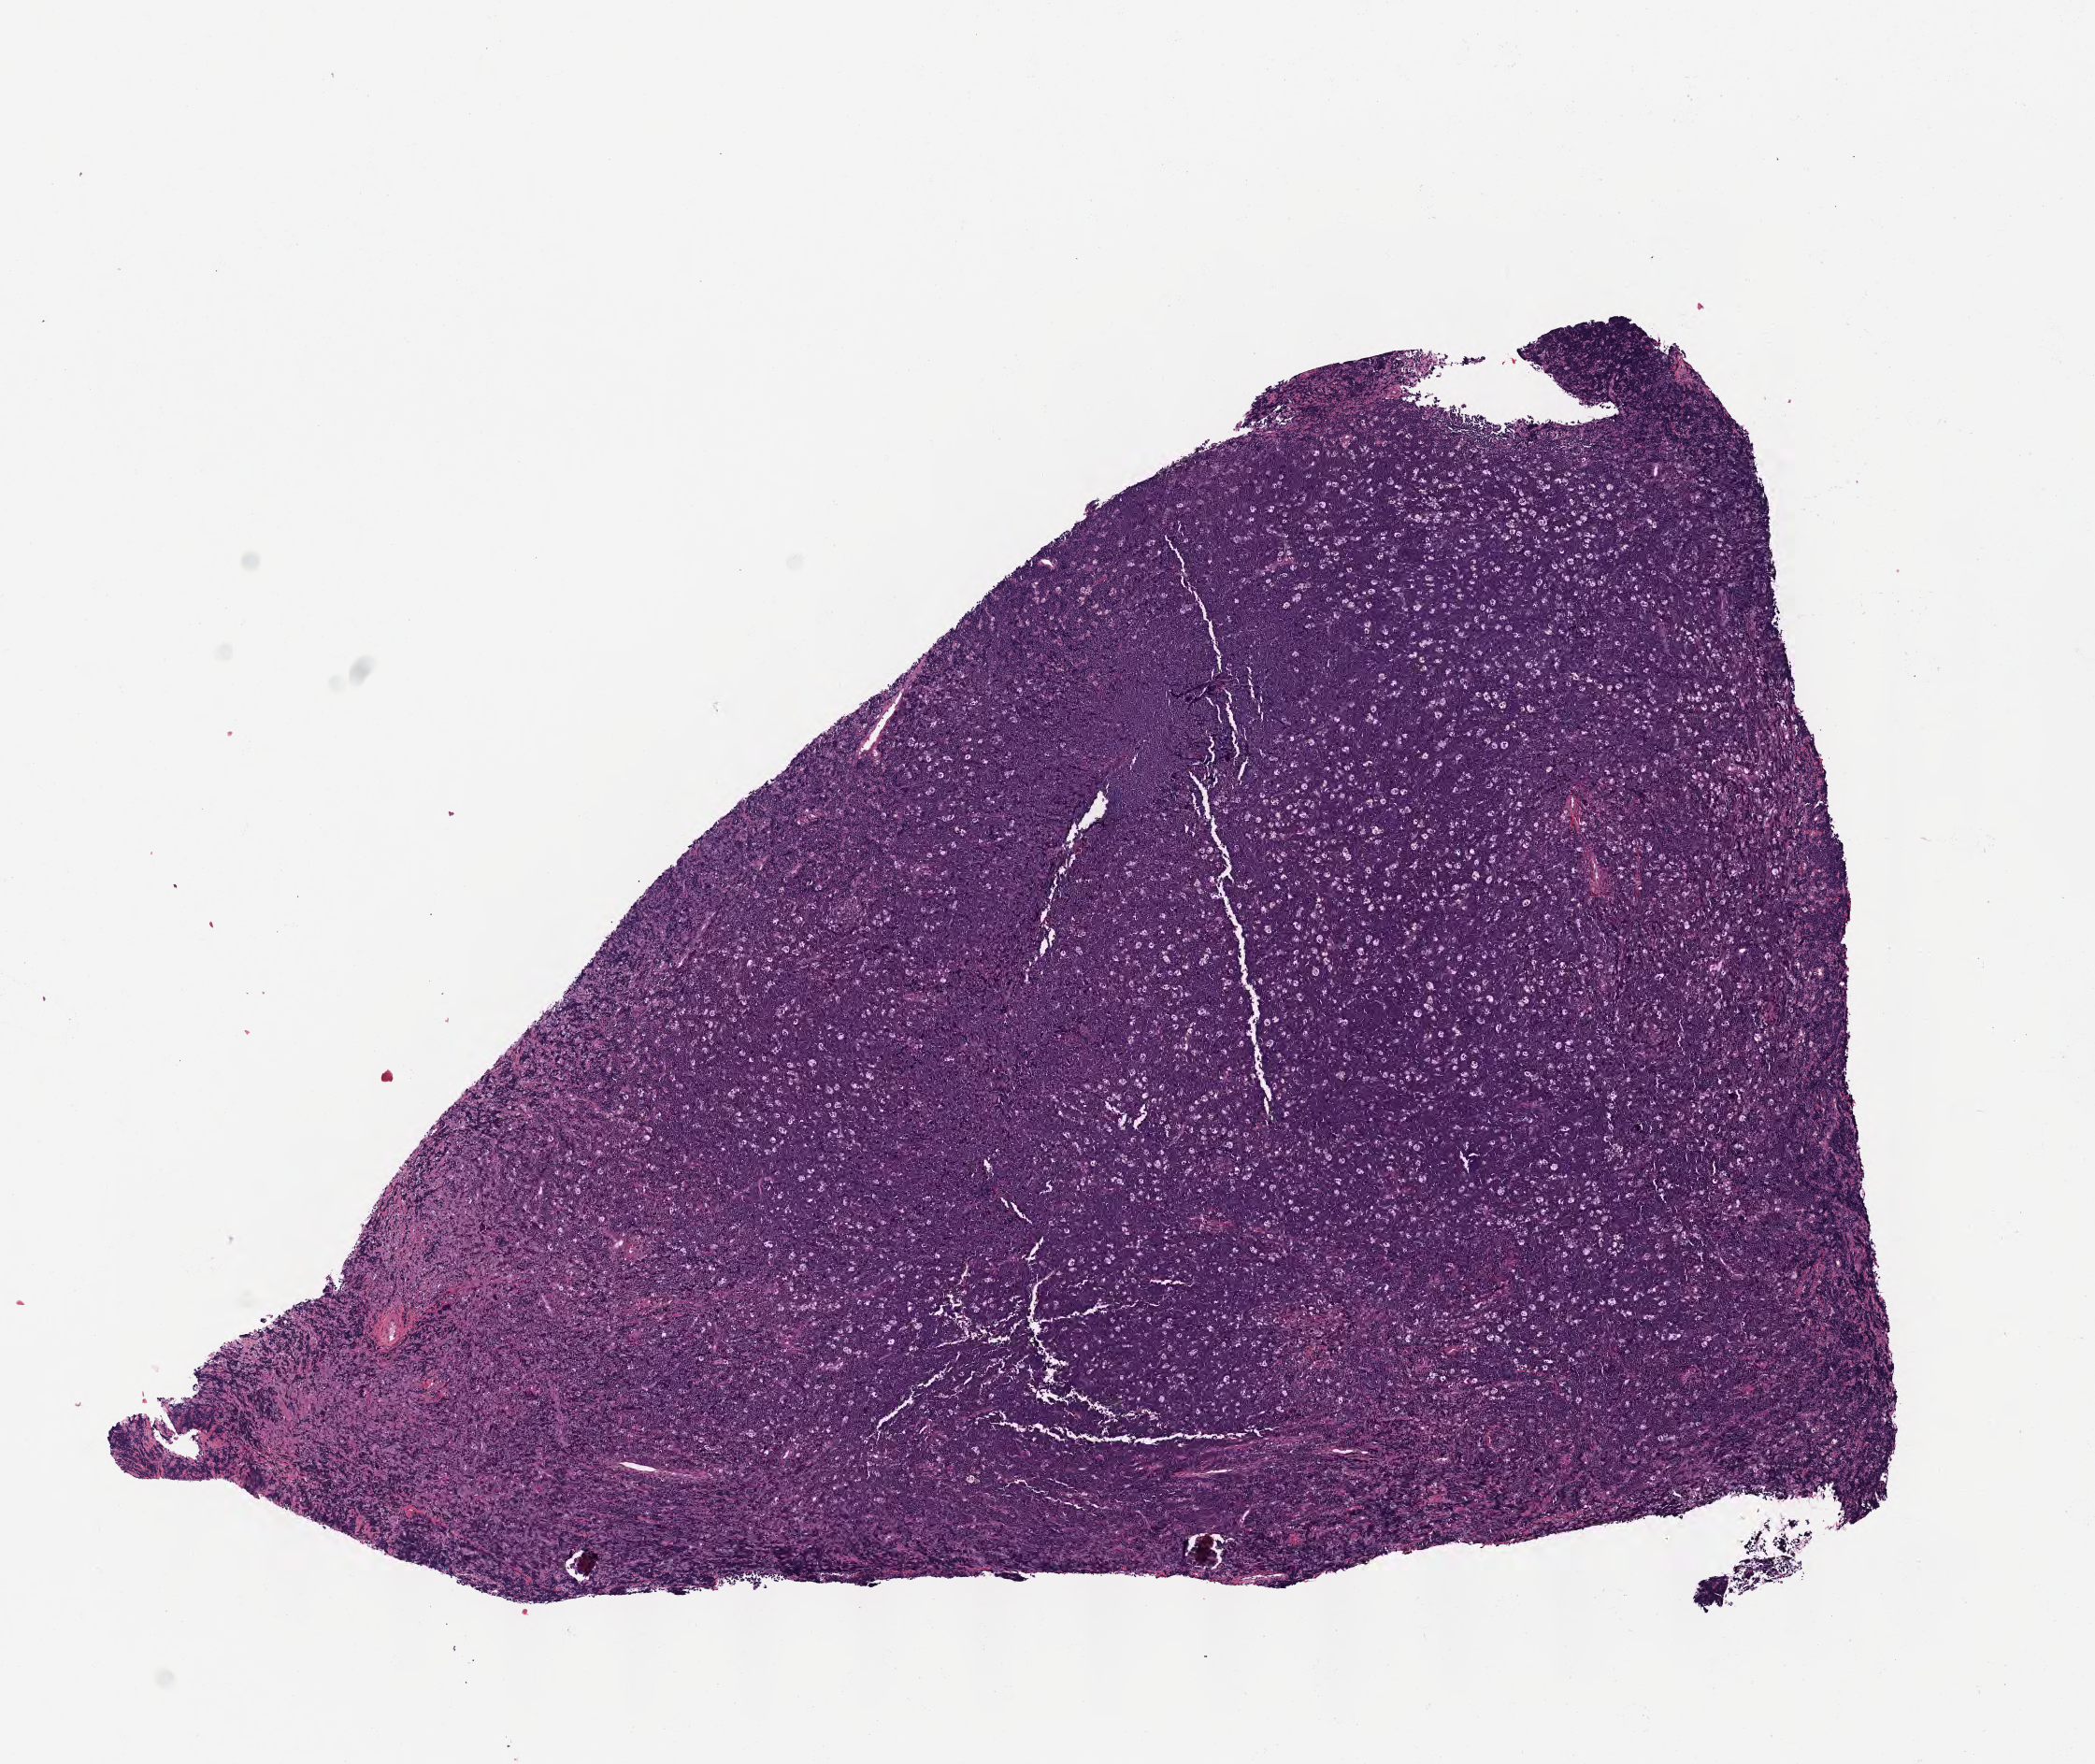
H&E whole-slide image, whole scanned area (about 9.1 x 7.6 mm) shown as a low-resolution overview; tumor tissue; site: cranium. Patient: male, age at initial diagnosis 9 years.
Histologic diagnosis: Burkitt lymphoma, NOS.